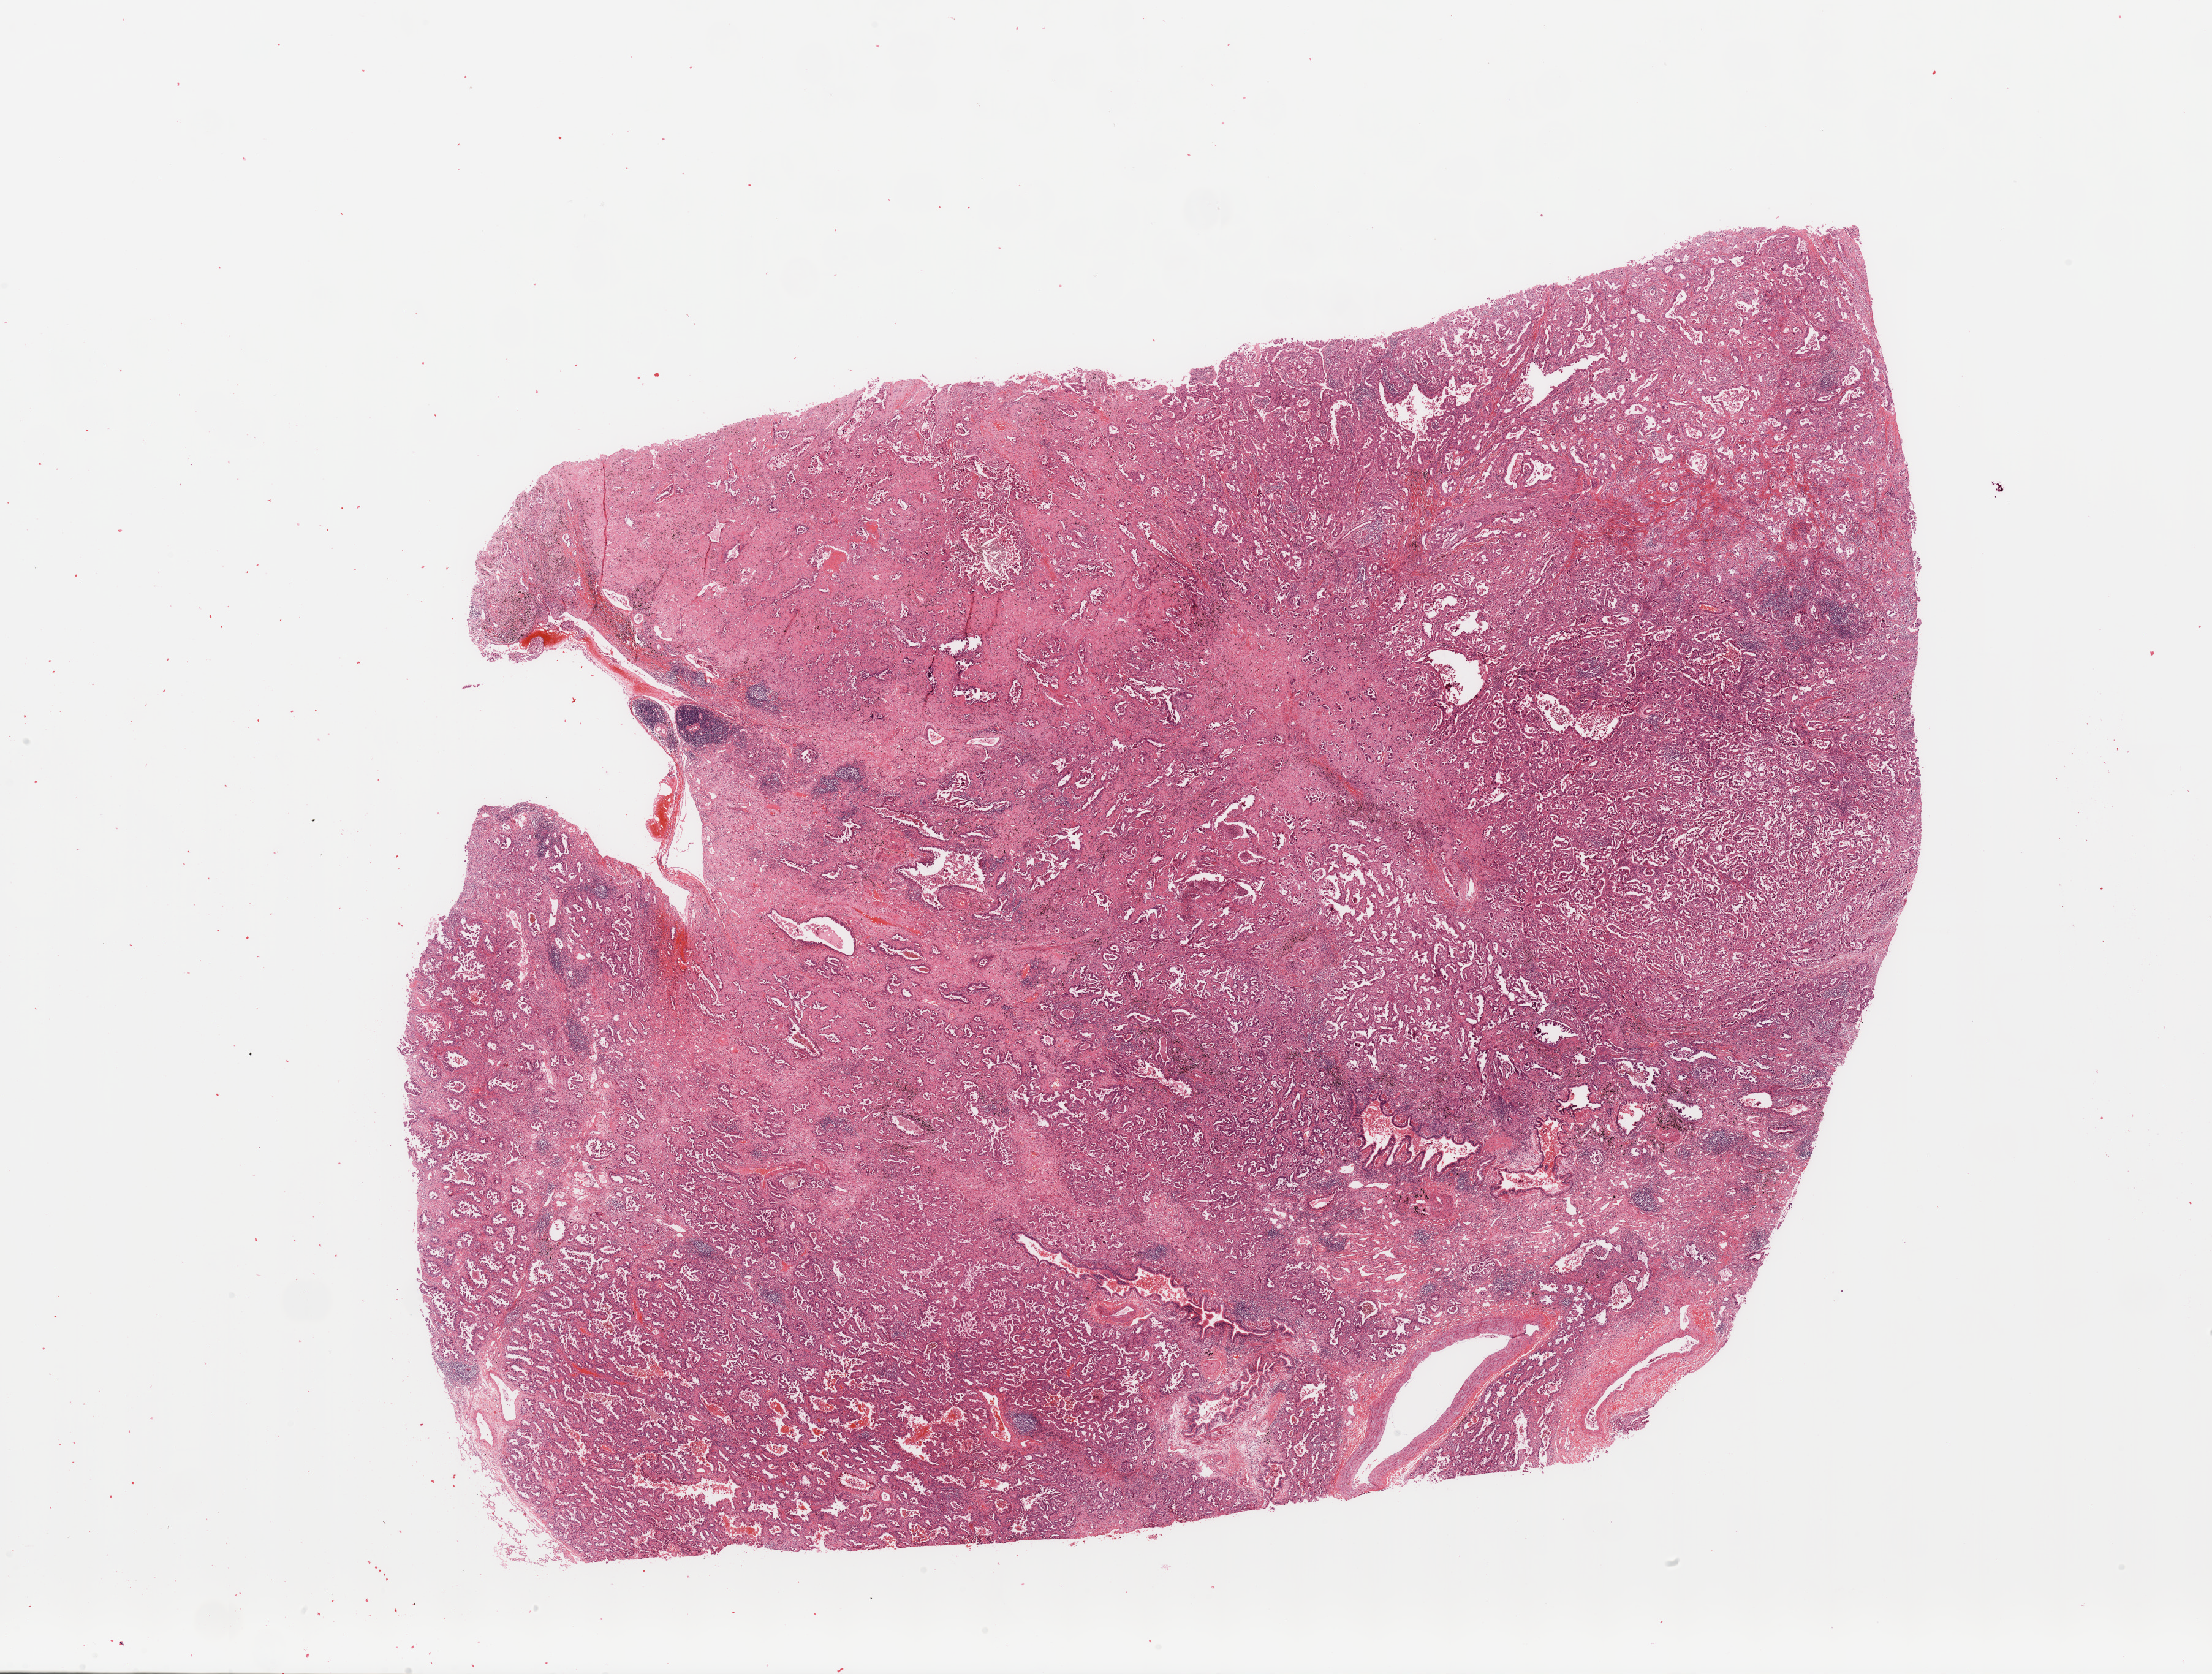
Digitized Hematoxylin and eosin (H&E) stained tissue section (whole slide) — low-resolution overview of the scanned area, about 28.5 x 21.6 mm (from a 20x scan). Lung, tumour tissue. Patient: female, age 72 years.
Histologic diagnosis: Adenocarcinoma, NOS.